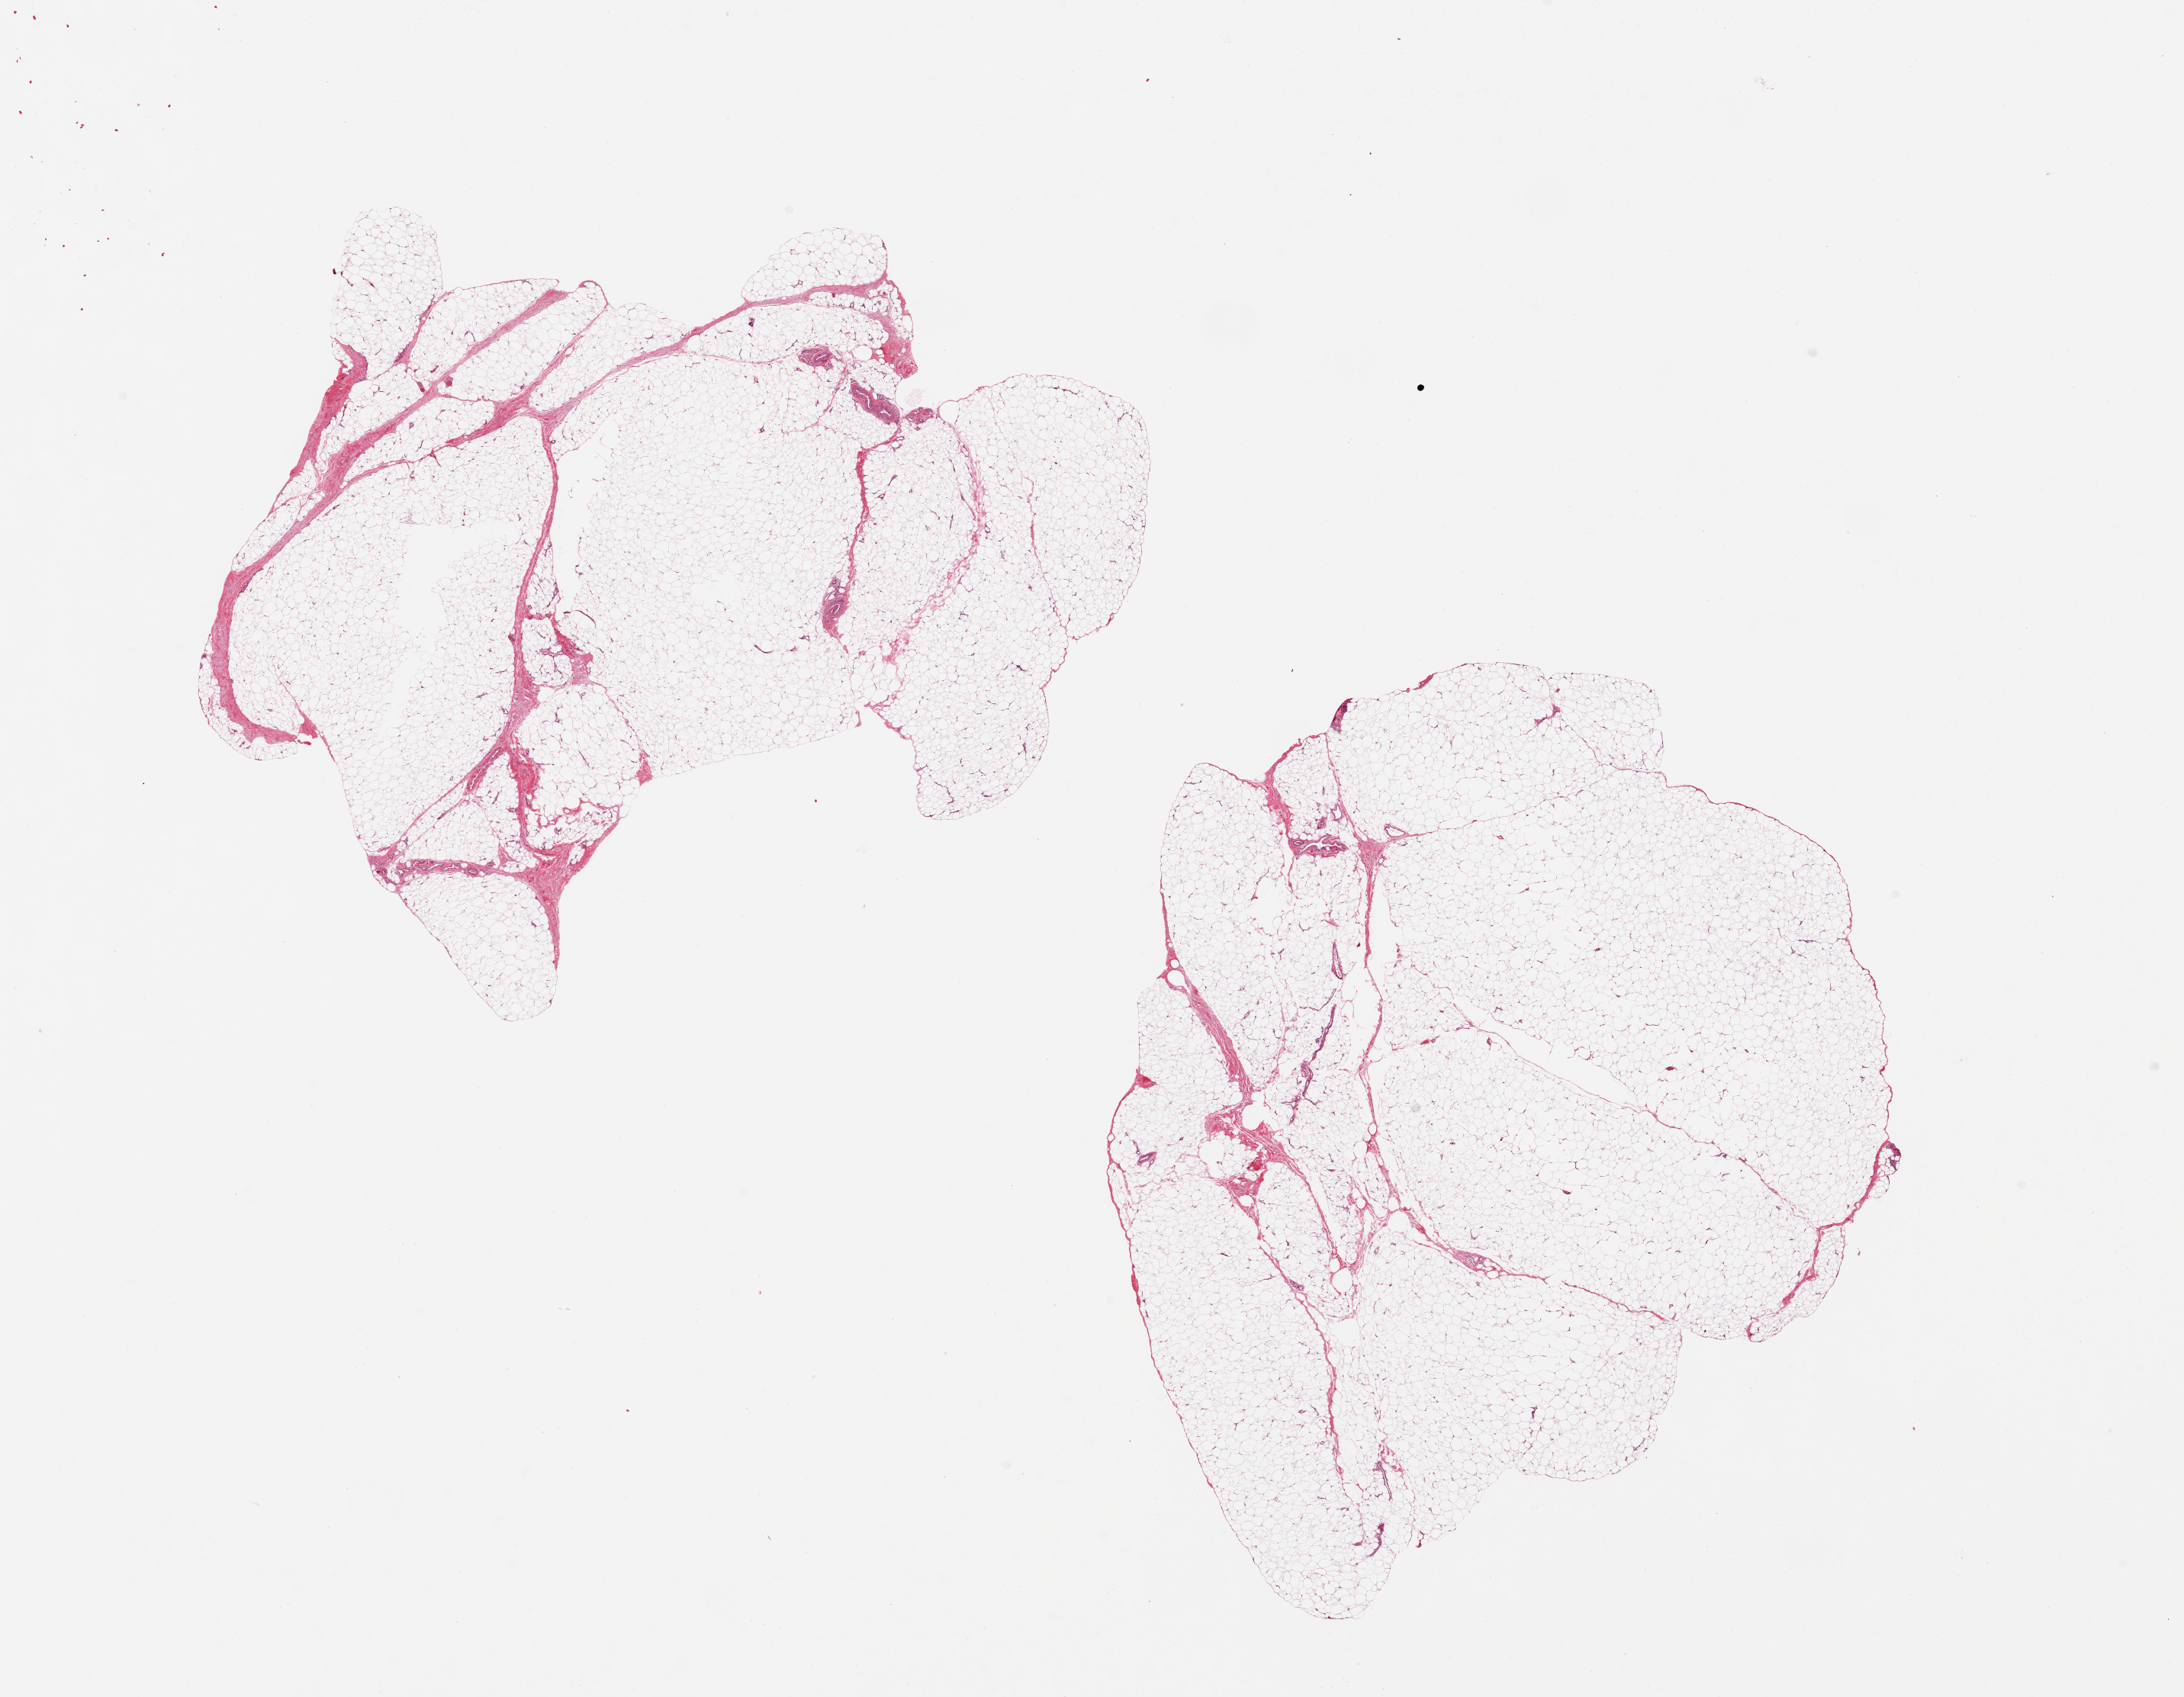
Hematoxylin and eosin (H&E) whole-slide image, shown as a low-resolution overview of the whole scanned area (about 22.6 x 17.6 mm); PAXgene-fixed, paraffin-embedded tissue; target tissue: adipose tissue; tissue donor sample.
Reviewer comment on this tissue sample: 2 pieces ~8x7mm.